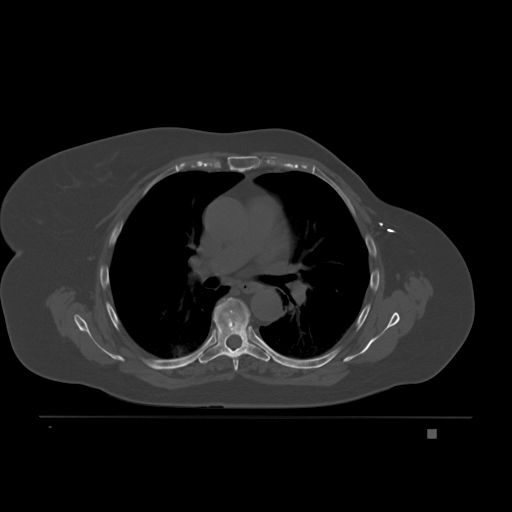
CT including the spine, one axial slice. Slice 139 of 221 in the series (ordered by position). Bone window (W 1800 / L 400 HU). 3 mm slice thickness. 512 × 512 image matrix, field of view 474 × 474 mm. Female patient, age 63 years. From the clinical record (not read from this slice): primary cancer: breast.
Outlined on this slice (semi-automatic segmentation, software-assisted and operator-edited):
- T5 vertebra: box from (x=208, y=345) to (x=239, y=372) px
- T6 vertebra: (x=198, y=297)–(x=270, y=364)